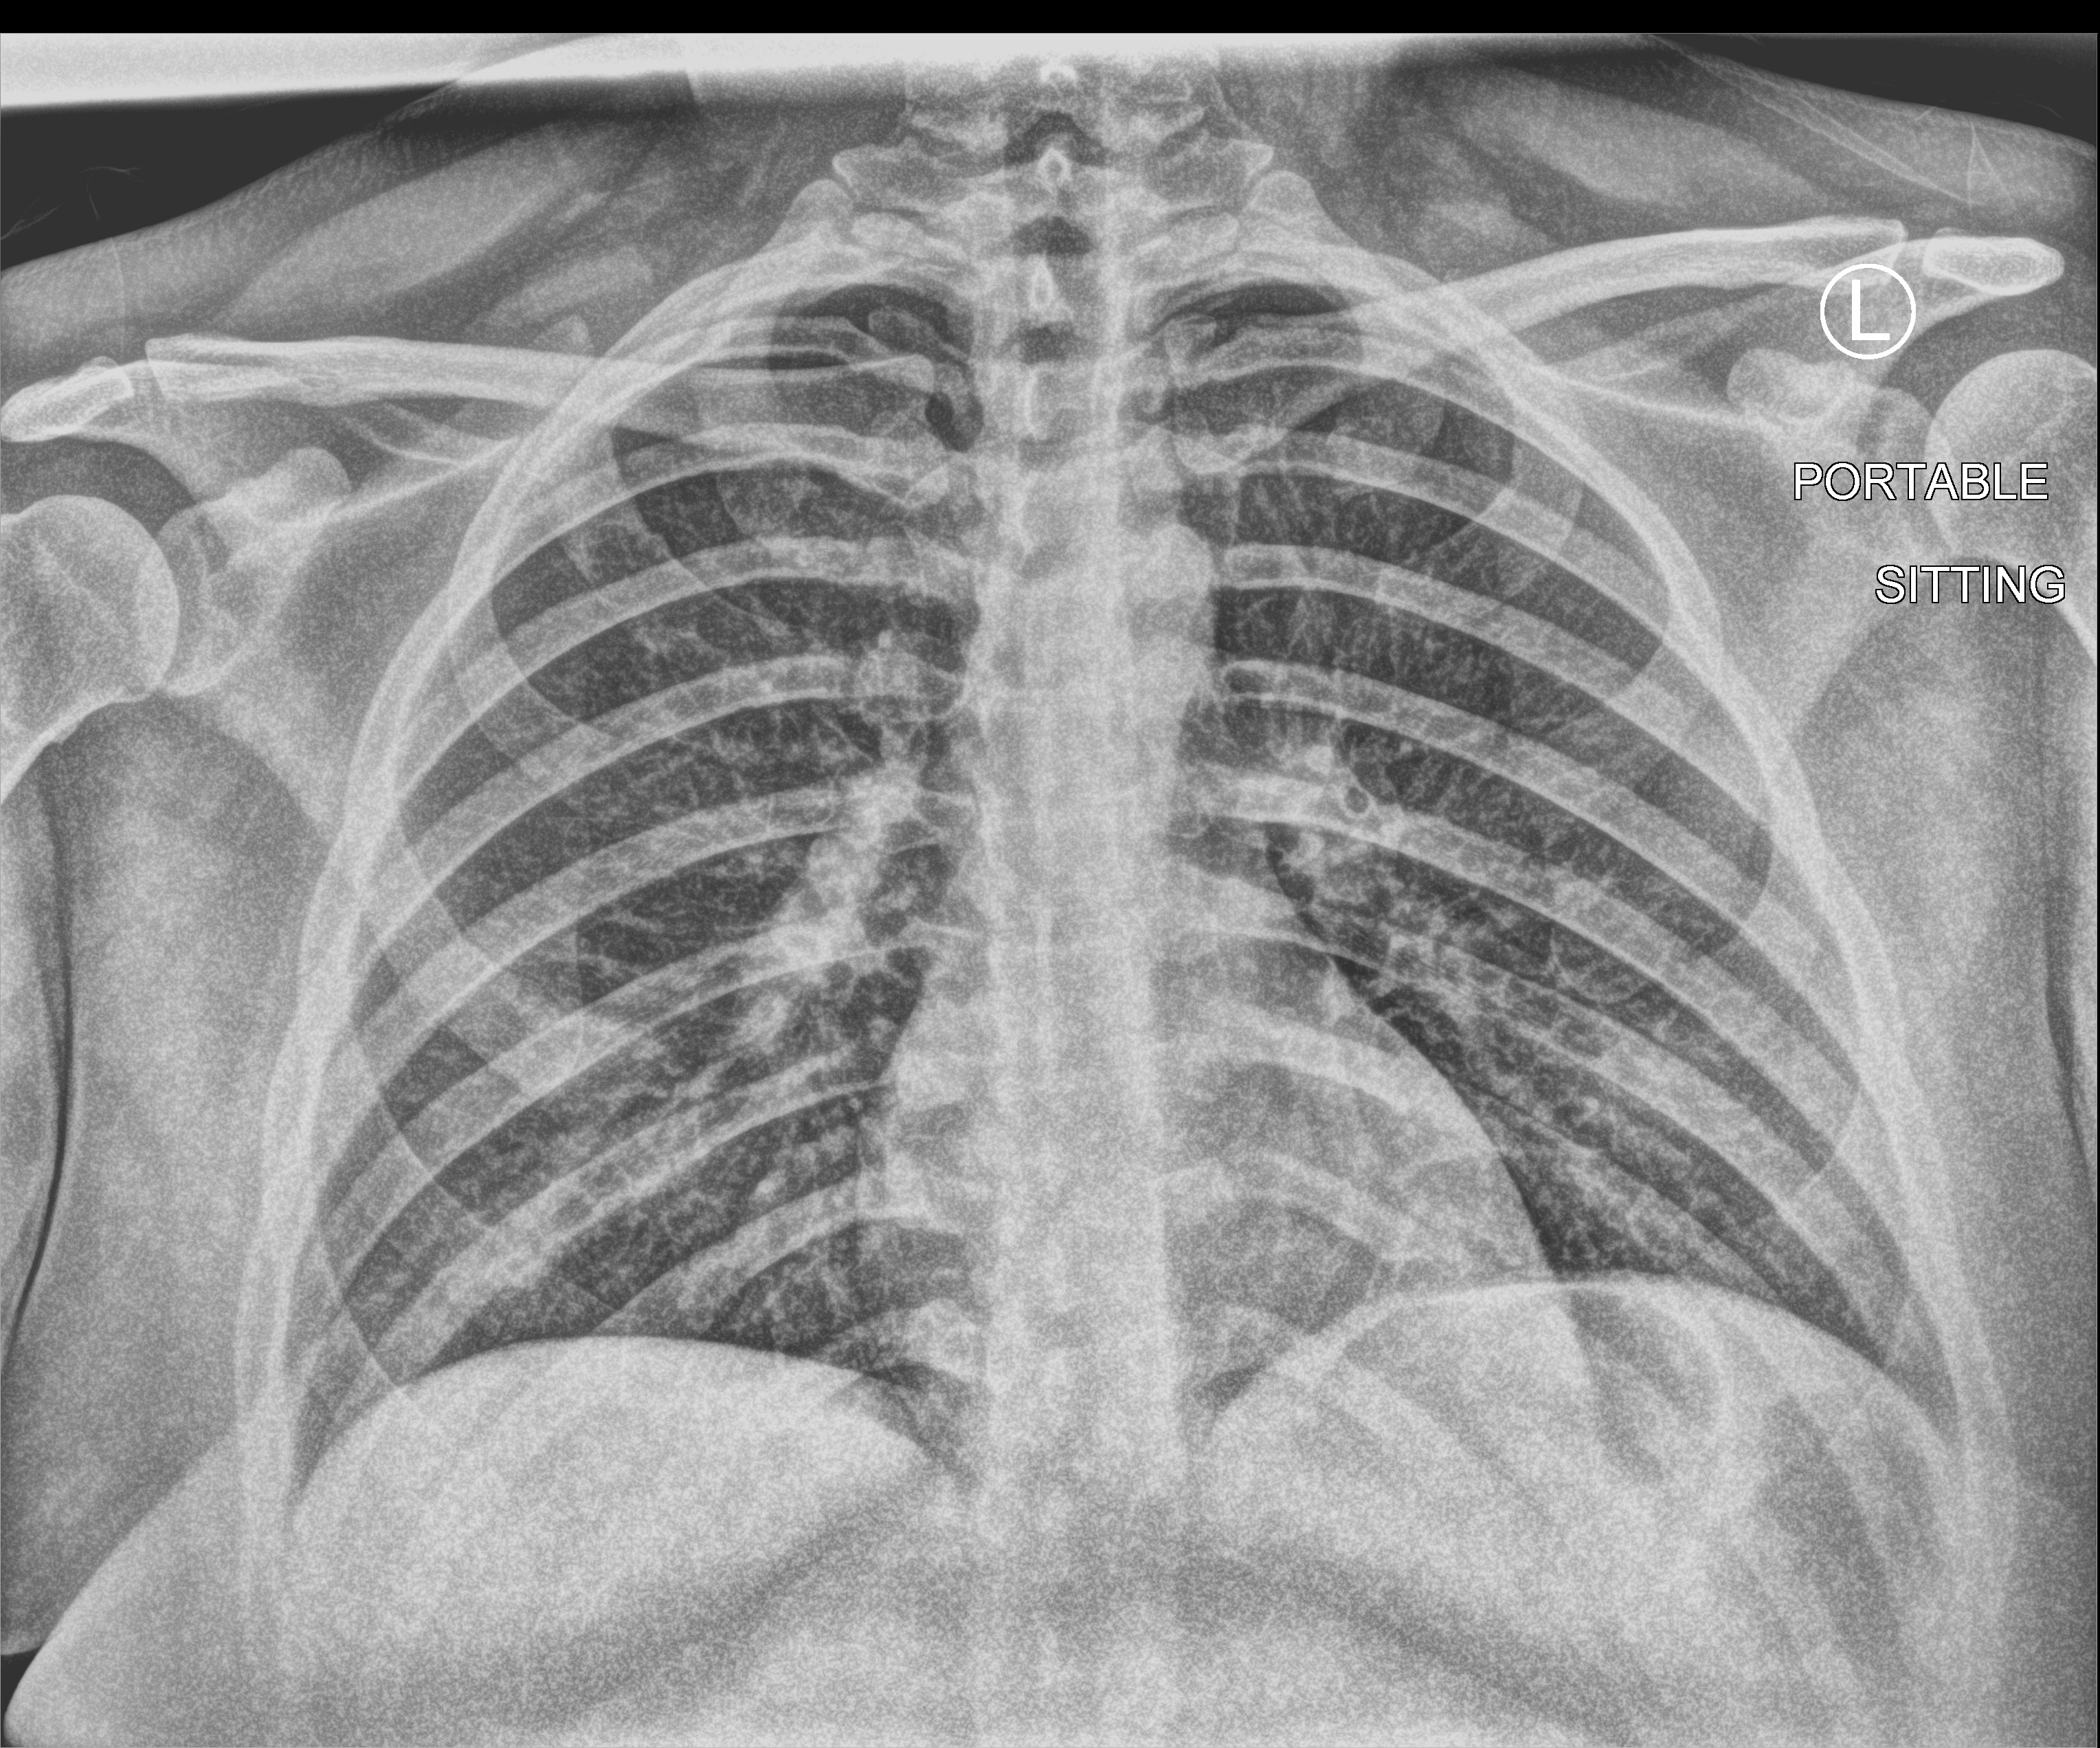
Portable chest radiograph, anteroposterior (AP) projection. Female patient hospitalised with COVID-19, age 18–59 years.
Hospital-stay facts (about this admission, not read from this image; timing relative to this image not recorded): mechanically ventilated during this hospital stay: no.